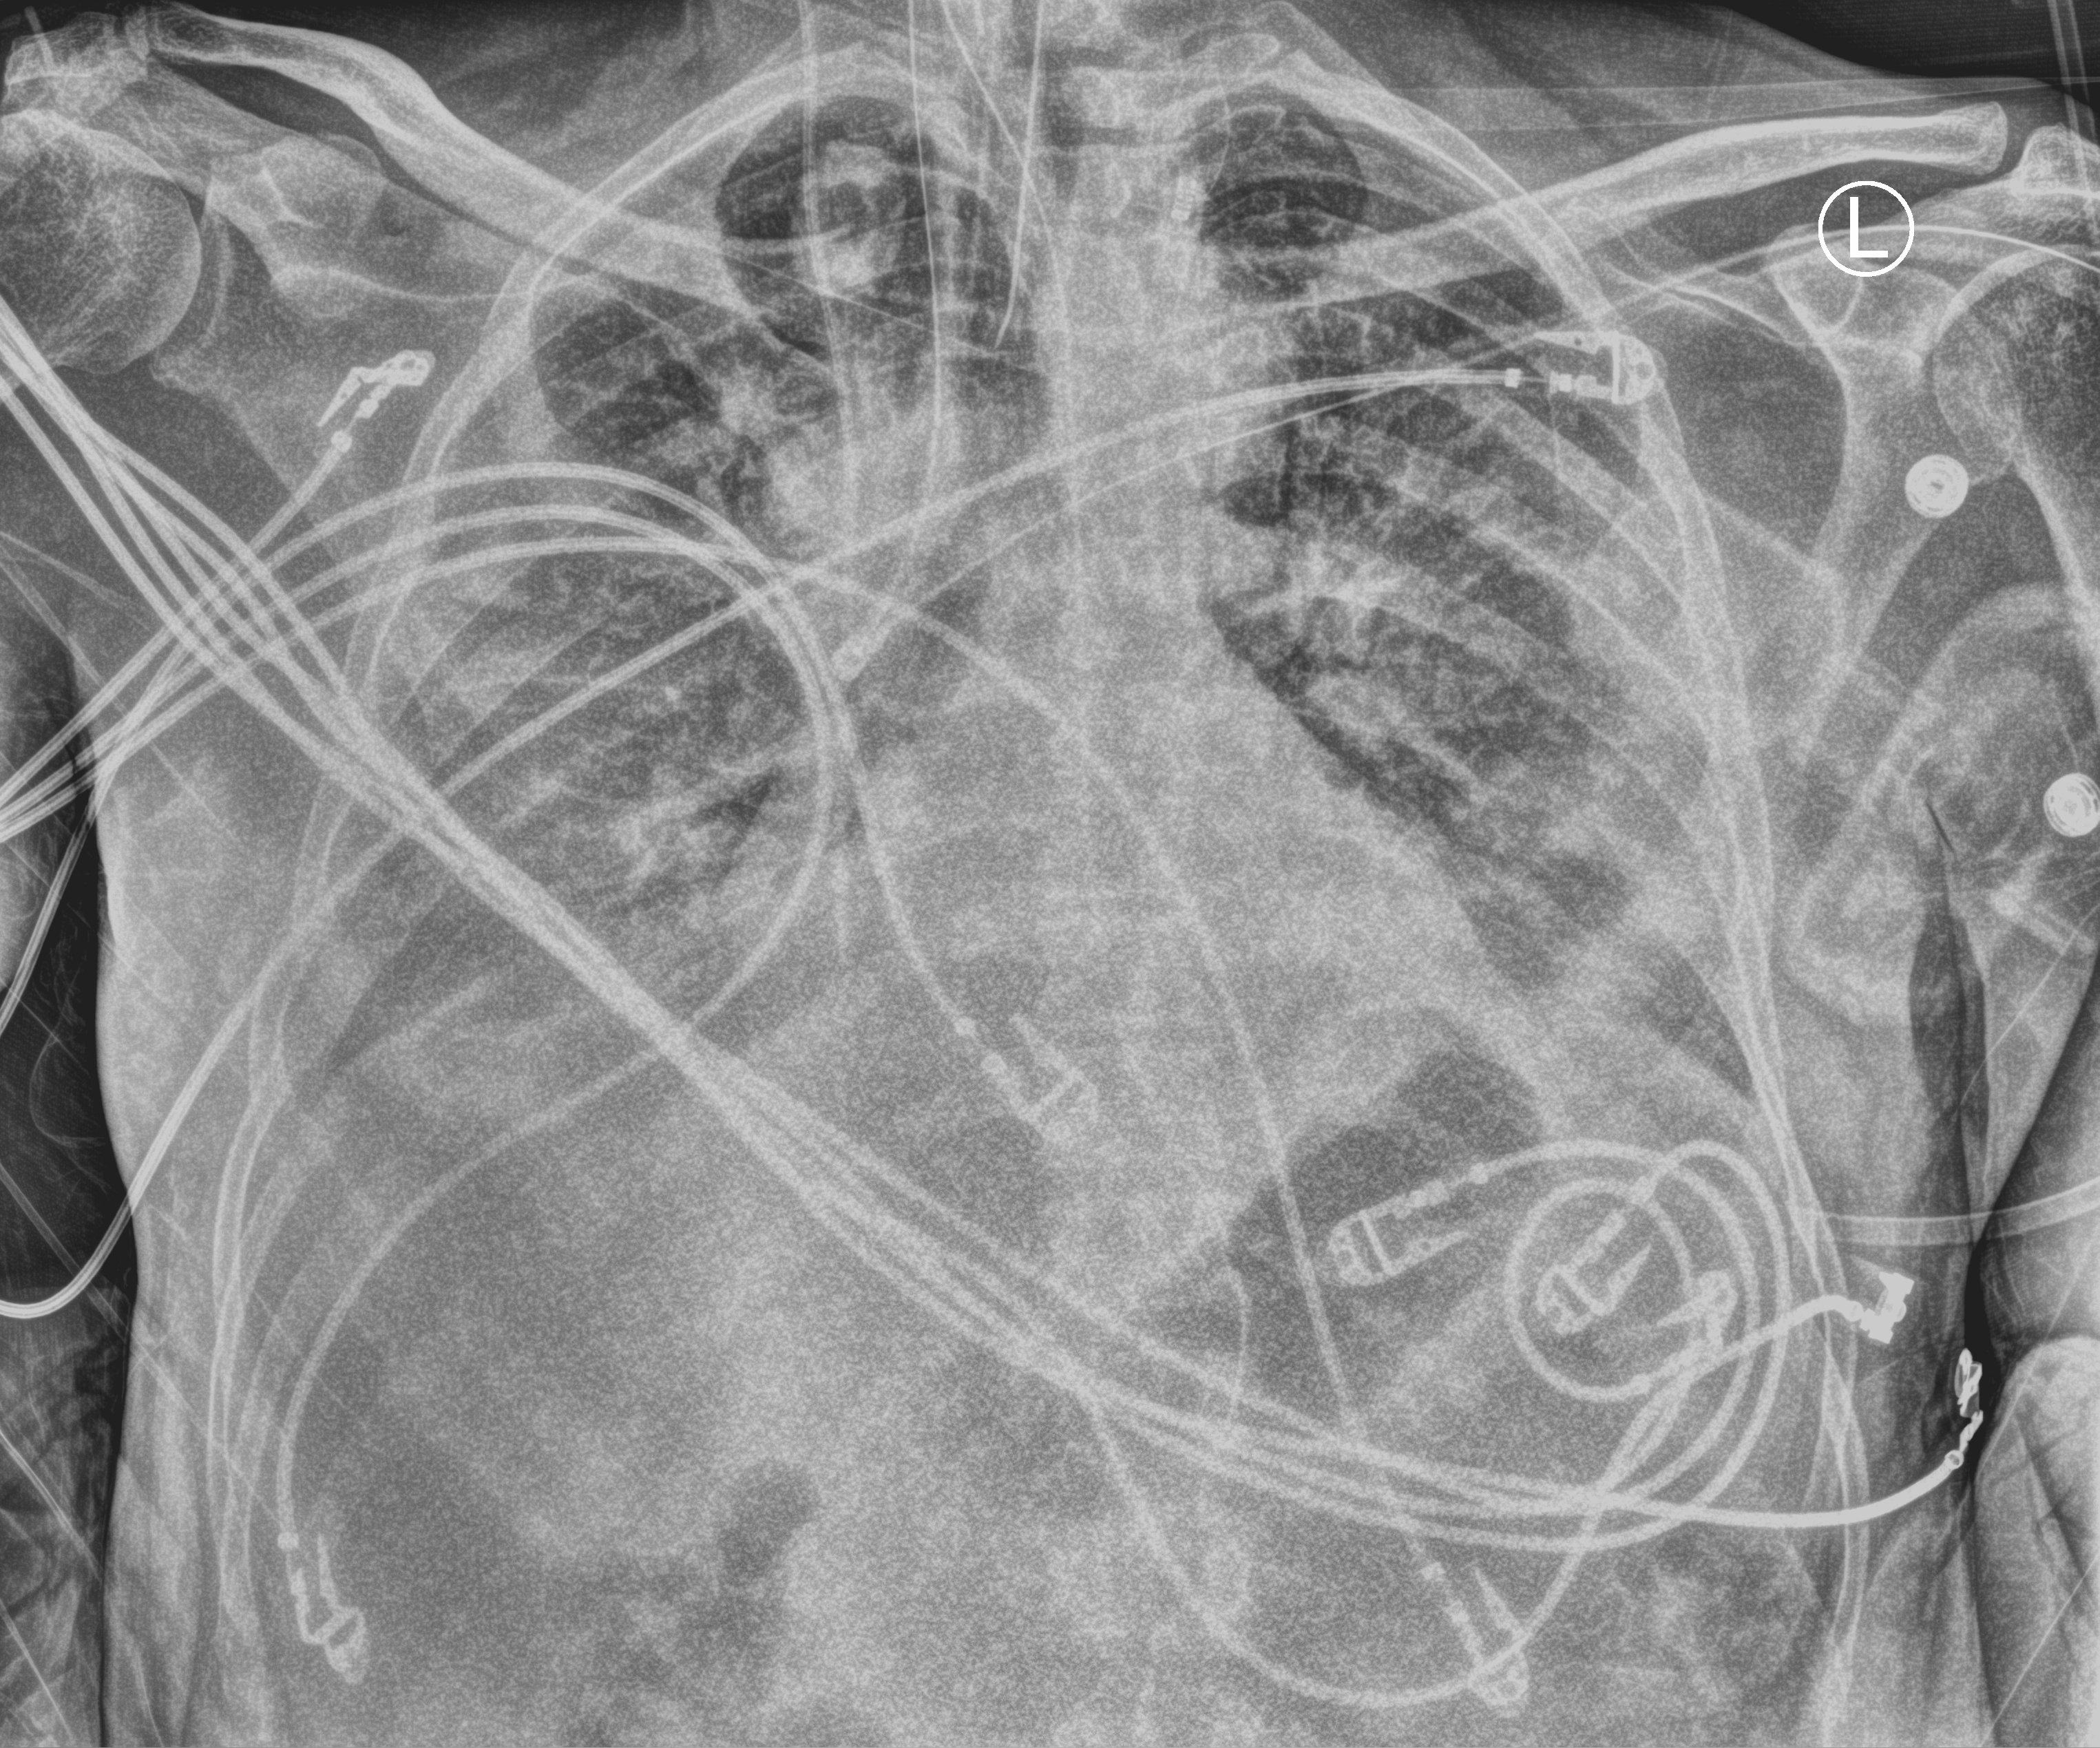
Bedside chest radiograph (computed radiography); anteroposterior (AP) projection. Patient hospitalised with COVID-19; male, aged 18–59 years.
Hospital-stay facts (about this admission, not read from this image; timing relative to this image not recorded): hypertension (admission record): no; chronic kidney disease (admission record): no.